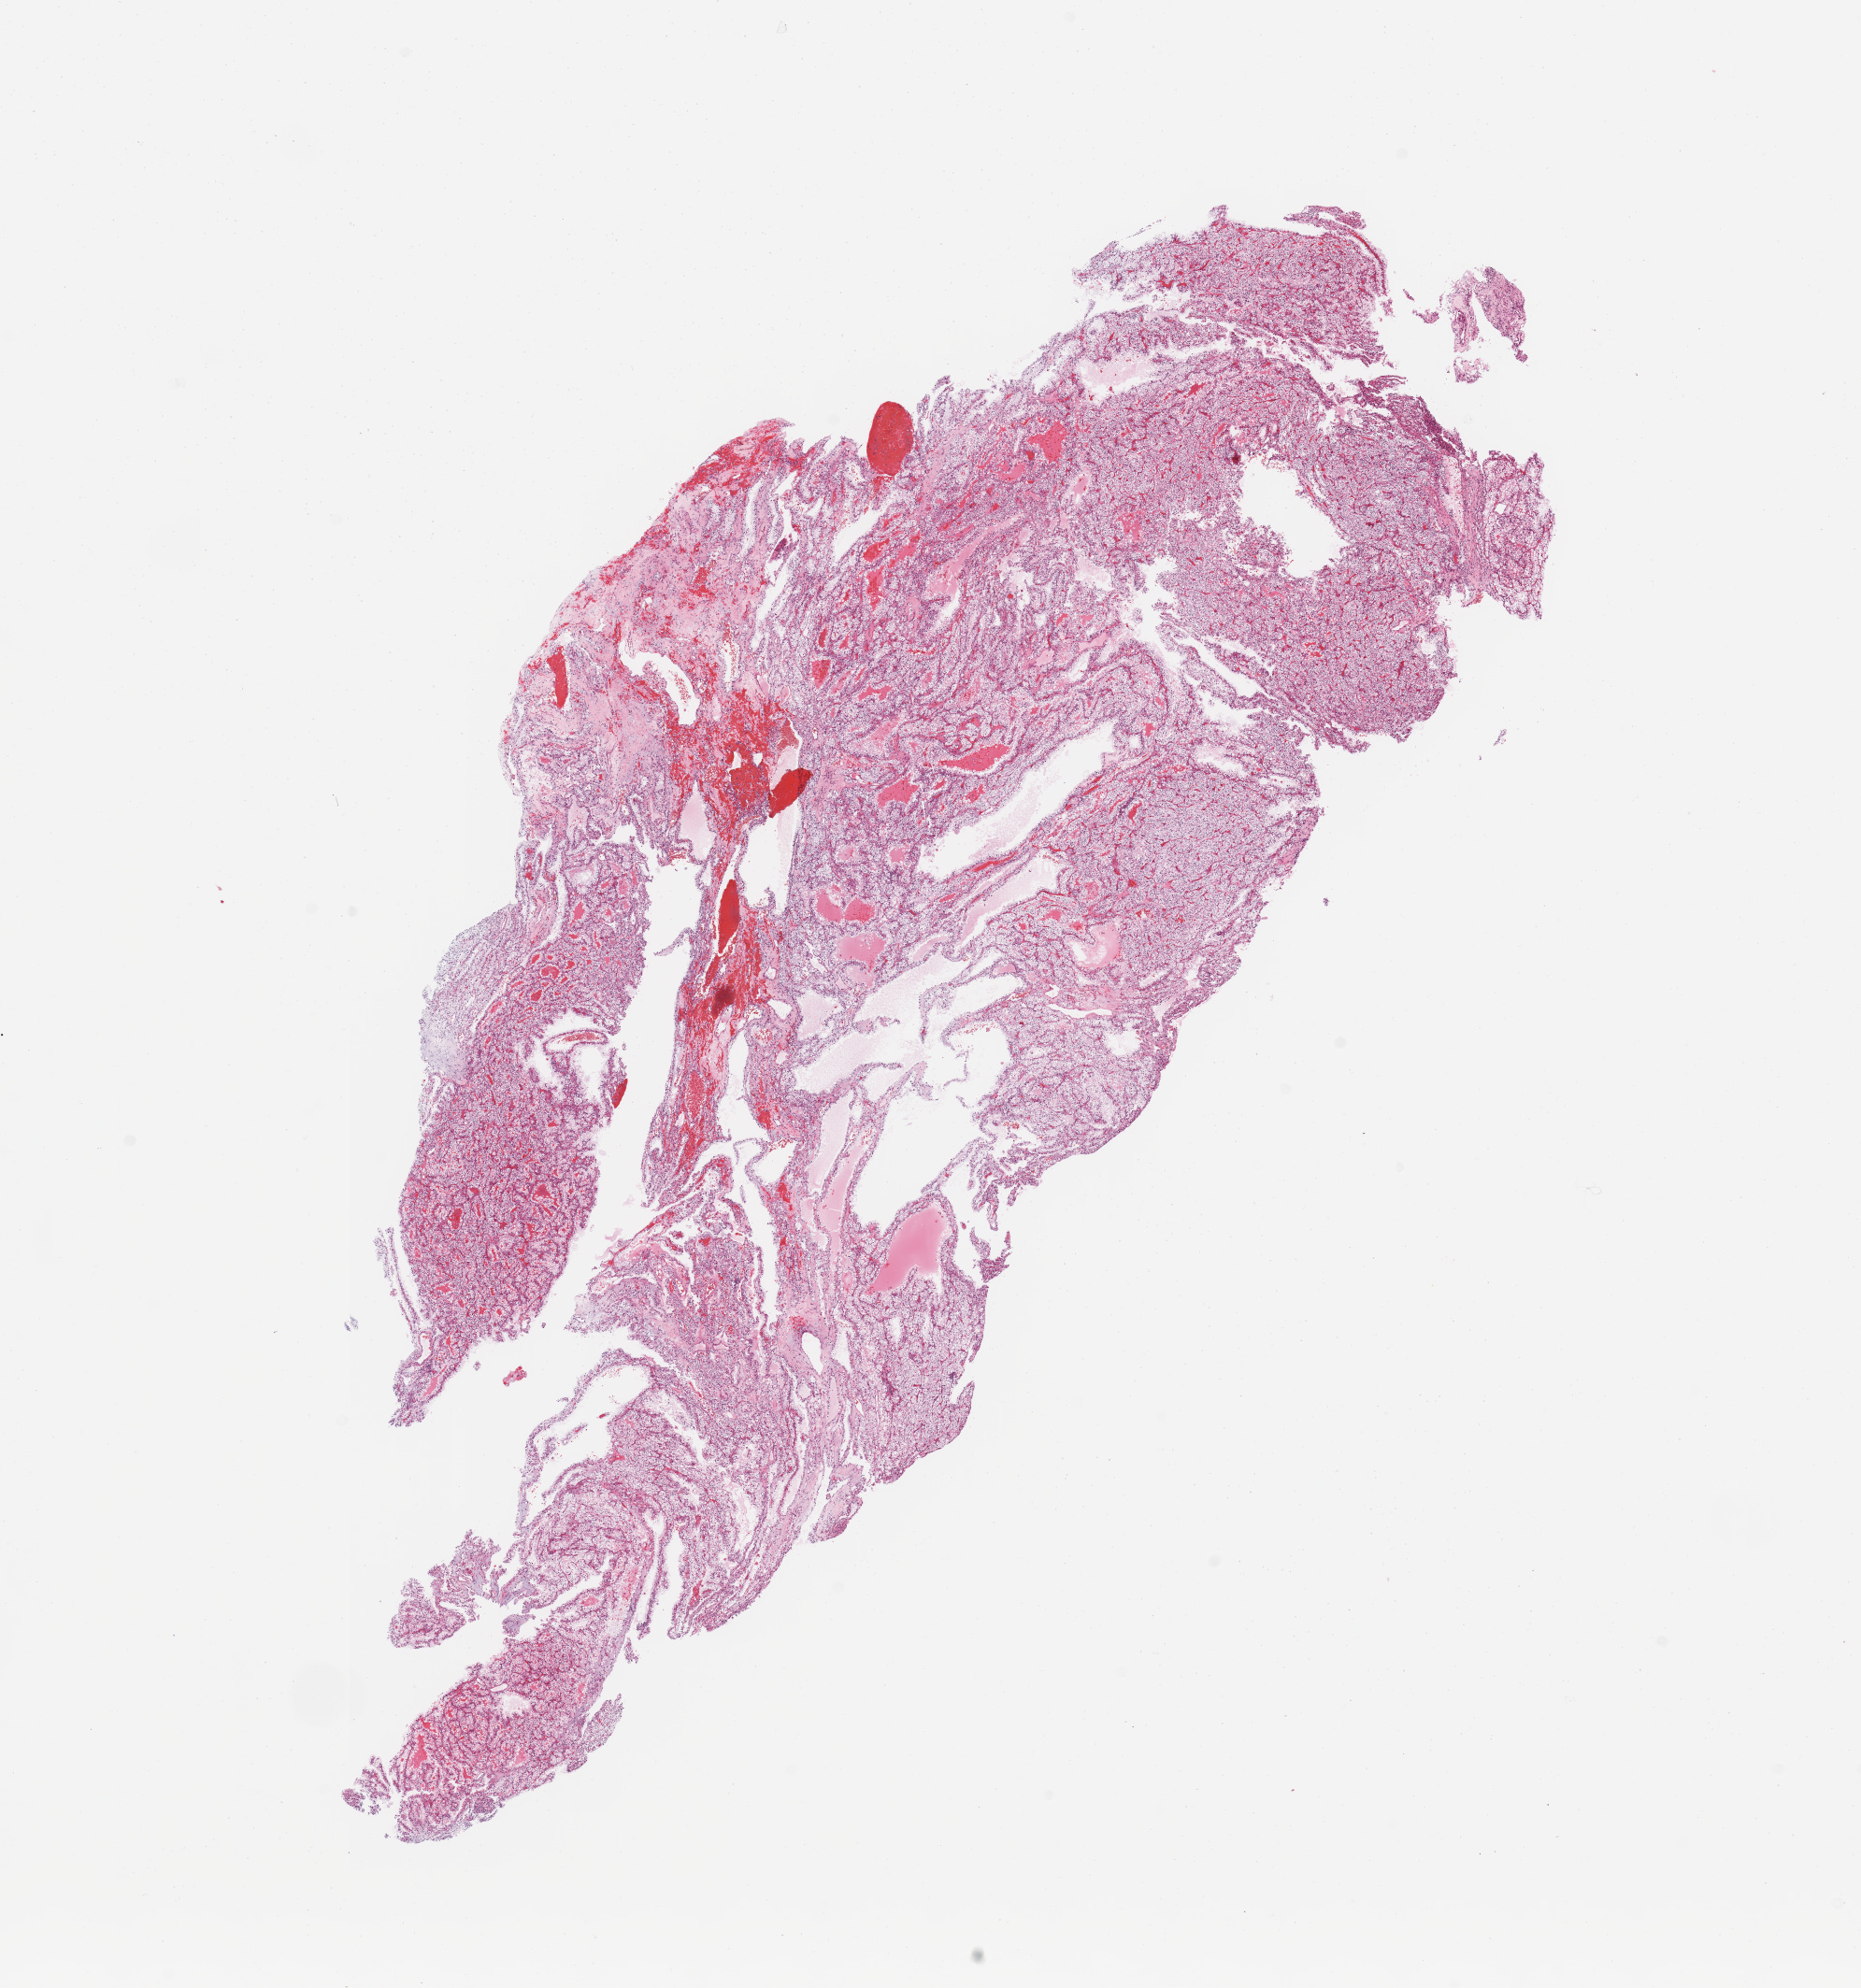
Hematoxylin and eosin (H&E) stained whole-slide image, low-resolution overview of the scanned area, about 15.8 x 16.8 mm, tumour tissue sample, sampled site: kidney. 55-year-old male patient. Histologic grade: G3 (poorly differentiated). Pathologist review of this section (percent, as recorded): tumour nuclei 90%, necrosis 0%.
Histologic diagnosis: Renal cell carcinoma, NOS. AJCC pathologic stage: I.